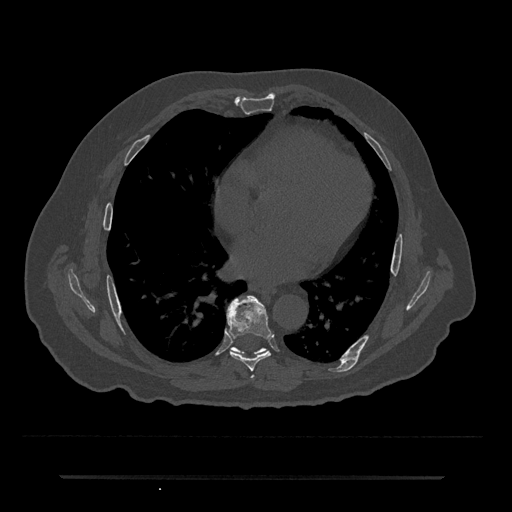
CT including the spine, one axial slice. Slice 370 of 797 in the series (ordered by position). 120 kVp. Bone window (W 1800 / L 400 HU). 512 × 512 image matrix, field of view 437 × 437 mm. Patient: male, 69 years. Case-level facts recorded for this patient, not image findings: primary cancer: prostate.
Outlined on this slice (semi-automatically segmented with operator editing):
- T7 vertebra: bounding box (x1, y1, x2, y2) in pixels: (226, 295, 272, 371)
- T8 vertebra: (230, 347, 266, 355)